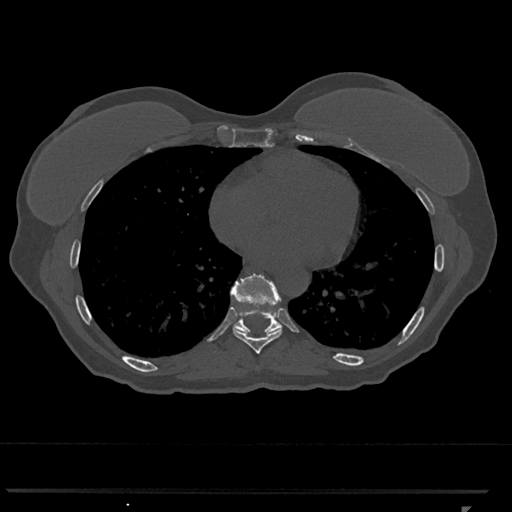
CT including the spine, one axial slice; 120 kVp; bone window (W 1800 / L 400 HU); 0.5 mm slice thickness; 512 × 512 image matrix, field of view 380 × 380 mm. Patient: female, 62 years. Case-level facts recorded for this patient, not image findings: primary cancer: renal.
Structures marked on this image (semi-automatically segmented with operator editing):
- T8 vertebra: bounding box (x1, y1, x2, y2) in pixels: (233, 328, 282, 354)
- T9 vertebra: (230, 274, 282, 335)